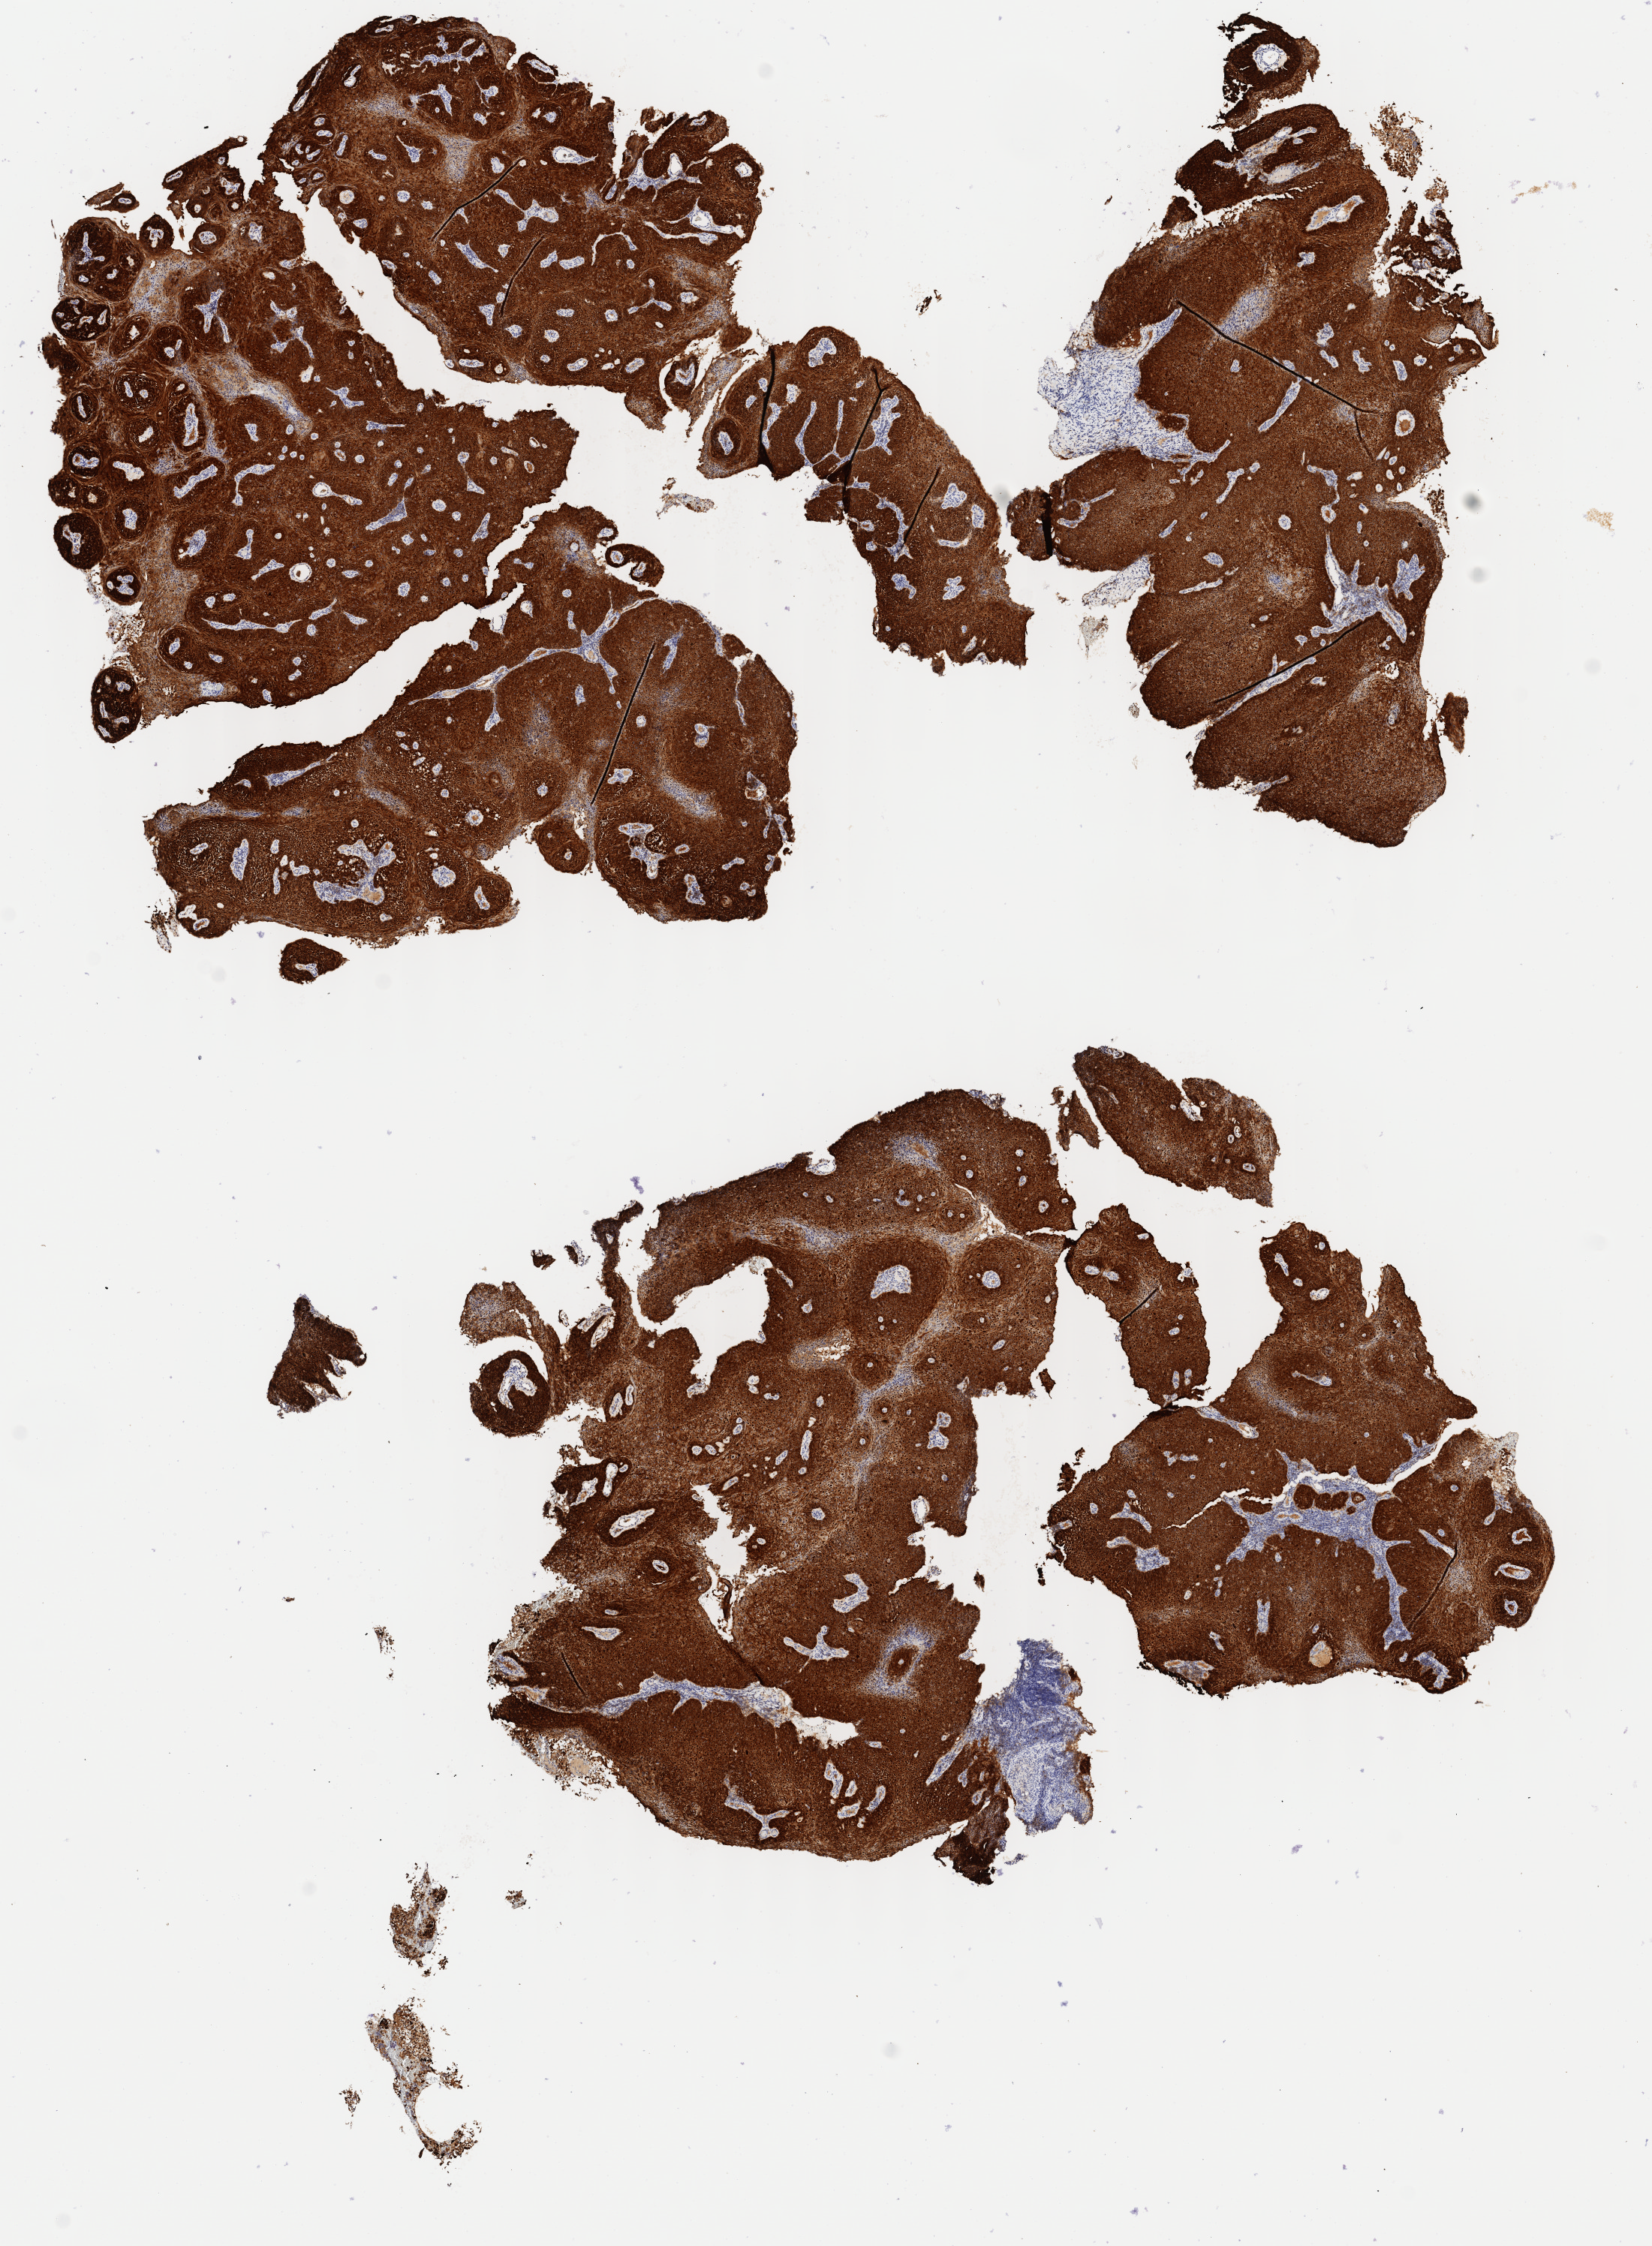
IHC for p16 (p16INK4a), whole-slide image — whole scanned area (about 8.8 x 11.9 mm) shown as a low-resolution overview; tumor tissue; anatomic site: cervix. Patient: female, age 45 years.
• diagnosis: Squamous cell carcinoma, keratinizing, NOS